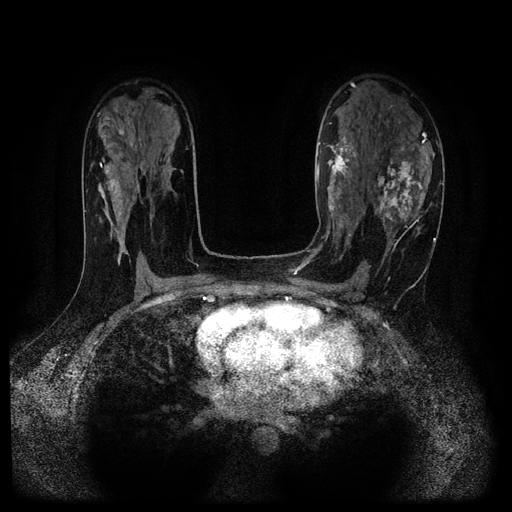
Breast MRI (dynamic contrast-enhanced, multi-phase), one axial slice. Position 65 of 116 along the scan axis. Dynamic contrast-enhanced series, time point 2 of 5 at this slice position (early post-contrast). 1.5 T. TE 2.7 ms, TR 5.4 ms. 2.2 mm slice thickness. 512 × 512 image matrix, field of view 330 × 330 mm. Patient: female, 43 years.
Outlined on this slice (semi-automatic segmentation, software-assisted and operator-edited):
- breast lesion (labelled 'tumour' in the annotation; benign lesions carry a separate 'benign' label): bounding box [x1, y1, x2, y2] px = [373, 159, 431, 229]
- breast lesion (labelled benign in the annotation): [326, 130, 356, 199]